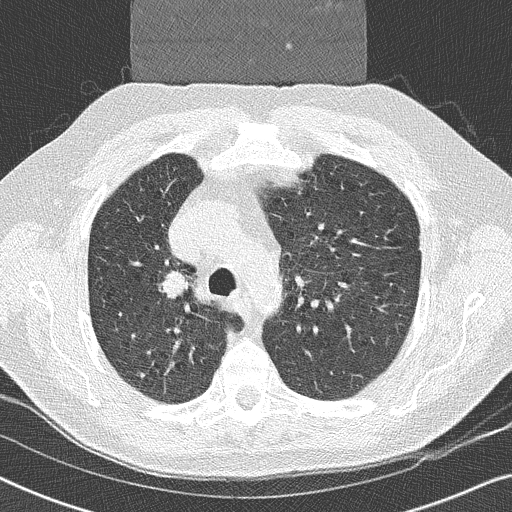
Low-dose screening chest CT, one axial slice; position 174 of 252 along the scan axis; 120 kVp; lung window (W 1500 / L -600 HU); 2 mm slice thickness; 512 × 512 image matrix, field of view 330 × 330 mm.
Outlined on this slice (expert manual segmentation):
- lesion 1 (tumor, upper lobe of right lung): bounding box (x1, y1, x2, y2) in pixels: (165, 271, 188, 298)